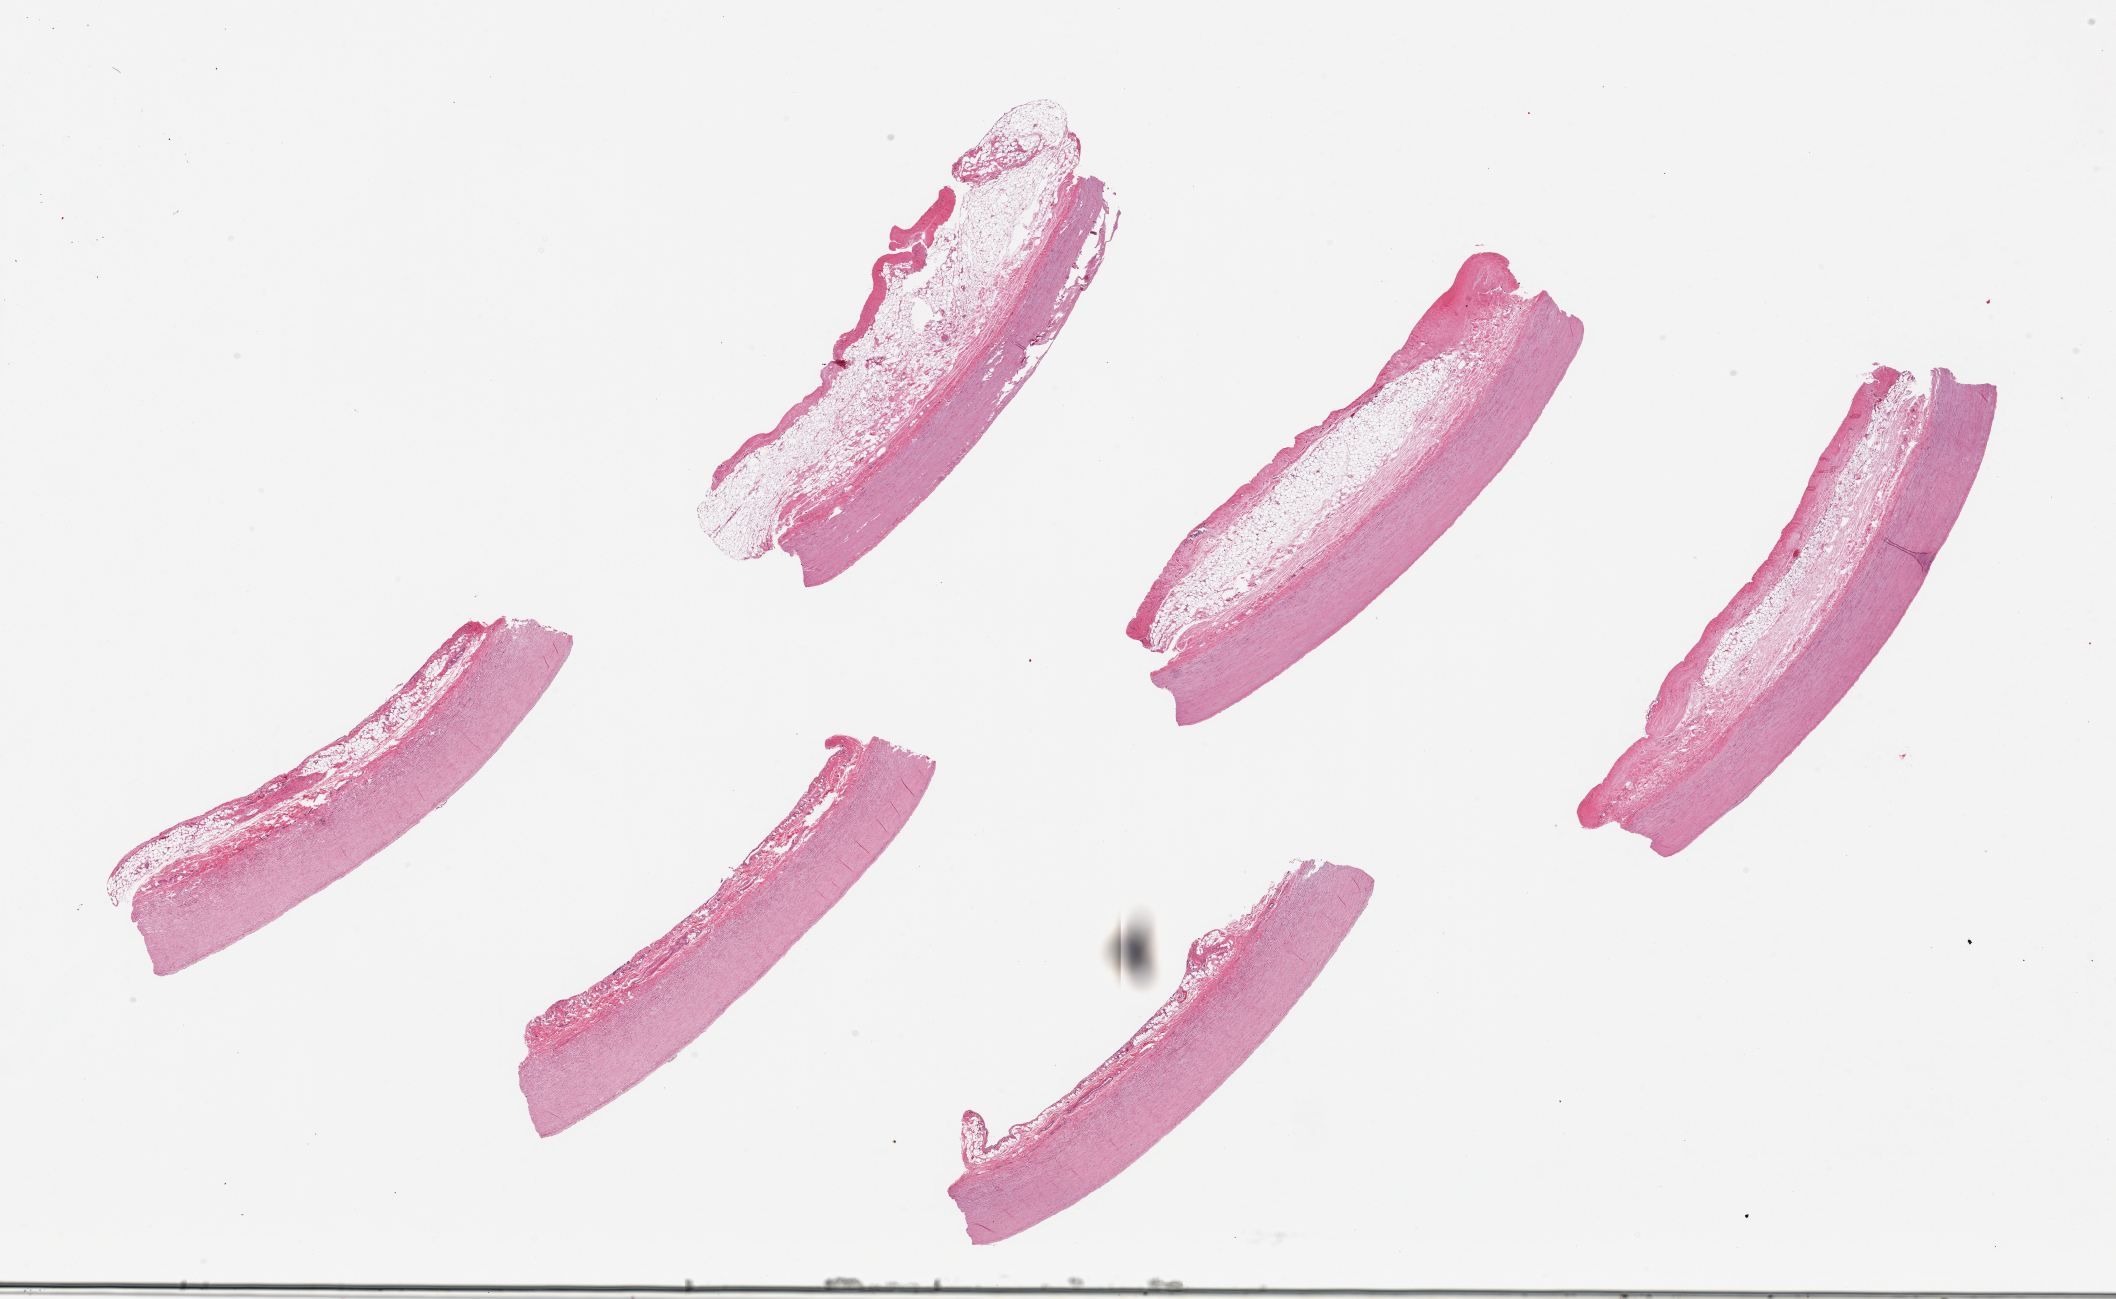
Whole-slide image, H&E stain — low-resolution overview of the scanned area, about 33.5 x 20.5 mm, PAXgene-fixed, paraffin-embedded tissue, section of aorta (target tissue), tissue donor sample. Female donor.
Pathologist's review note for this sample: 6 pieces, ~8.5x1mm; 4 of 6 have ~1.5mm layer of adherent fibroadipose tissue.